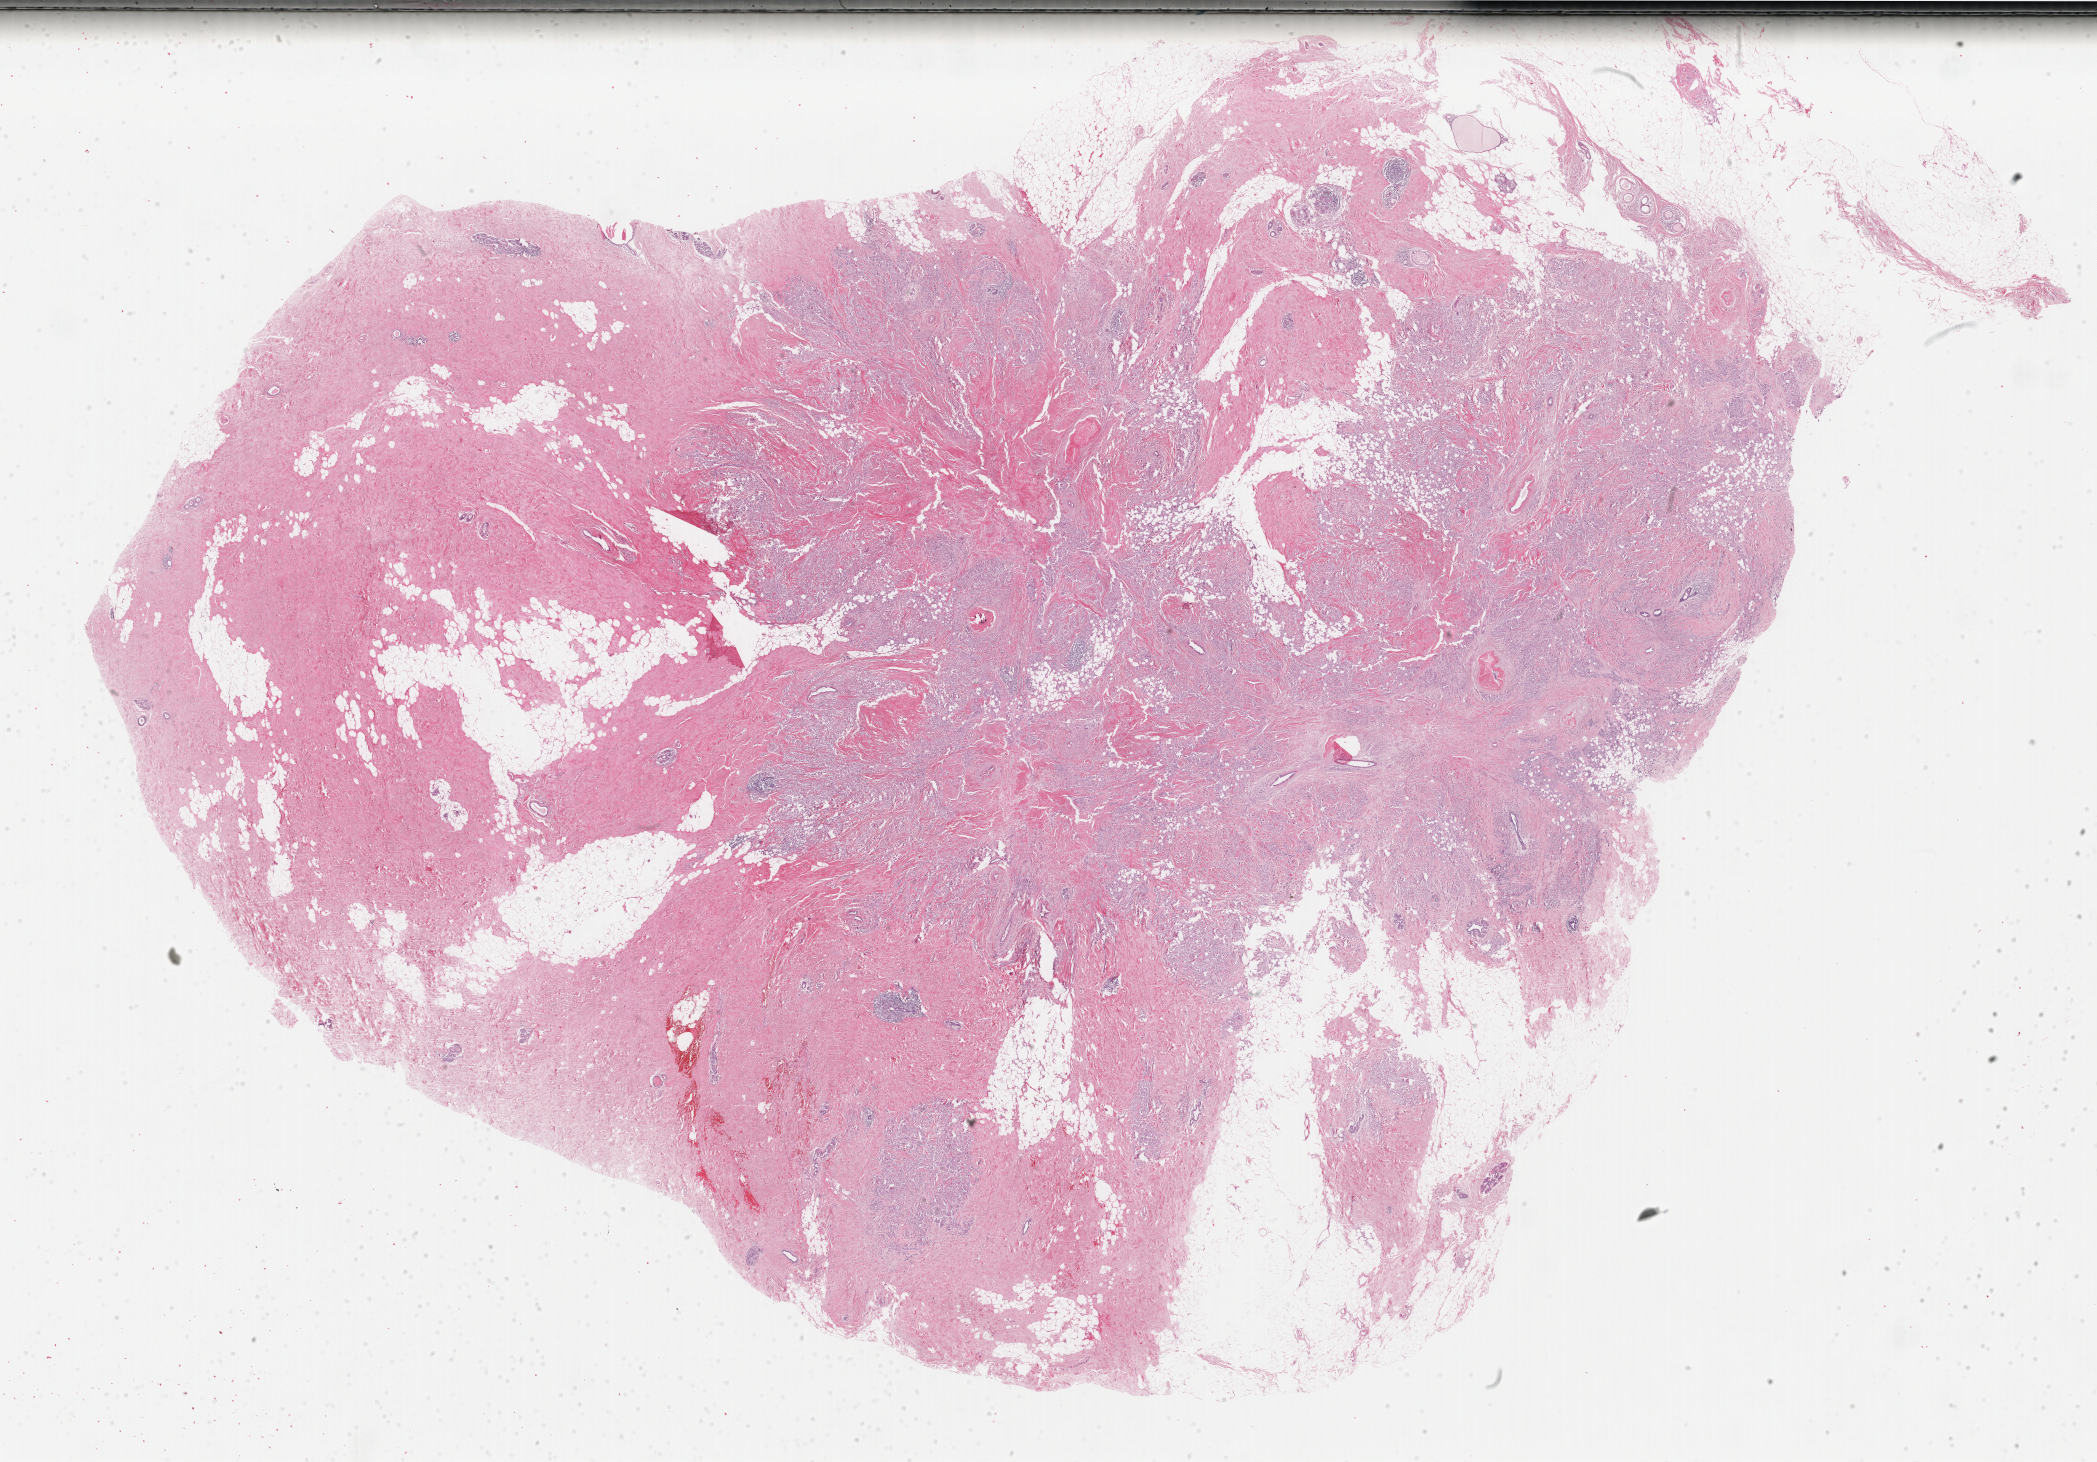
Whole-slide histology image, H&E-stained, a low-resolution overview of the entire scanned area, about 33.3 x 23.2 mm; FFPE section; primary tumour sample from the breast. Female, age 62 years at initial diagnosis.
Histologic diagnosis: Lobular carcinoma, NOS.